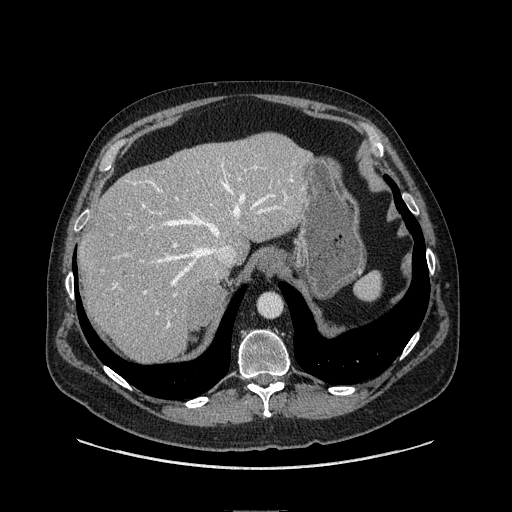
Contrast-enhanced abdominal CT, one axial slice. Slice 90 of 149 in the series (ordered by position). Soft-tissue window (W 400 / L 40 HU). 1.25 mm slice thickness. 512 × 512 image matrix, field of view 440 × 440 mm. Male patient. Case-level facts recorded for this patient, not image findings: diagnosis: adrenocortical carcinoma; tumour side: right adrenal; tumour size at pathology: 7.5 cm; Ki-67 index: 15 %; stage (as recorded): 2.
Annotated regions visible in this slice (semi-automatic segmentation, software-assisted and operator-edited):
- mass: box from (x=190, y=285) to (x=225, y=327) px